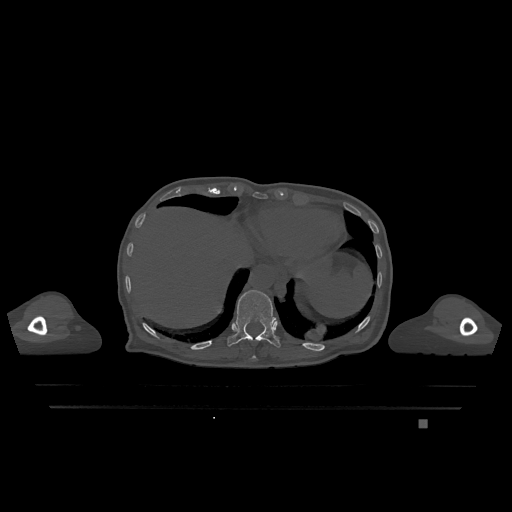
CT including the spine, one axial slice; bone window (W 1800 / L 400 HU); 512 × 512 image matrix, field of view 500 × 500 mm. Female patient, age 74 years. Case-level facts recorded for this patient, not image findings: primary cancer: lung; vertebrae with lytic lesions (as recorded): T1, T4, T5, T6, L4, L5.
Annotated regions visible in this slice (semi-automatic segmentation, software-assisted and operator-edited):
- T10 vertebra: box from (x=250, y=355) to (x=258, y=360) px
- T11 vertebra: (x=227, y=290)–(x=281, y=348)